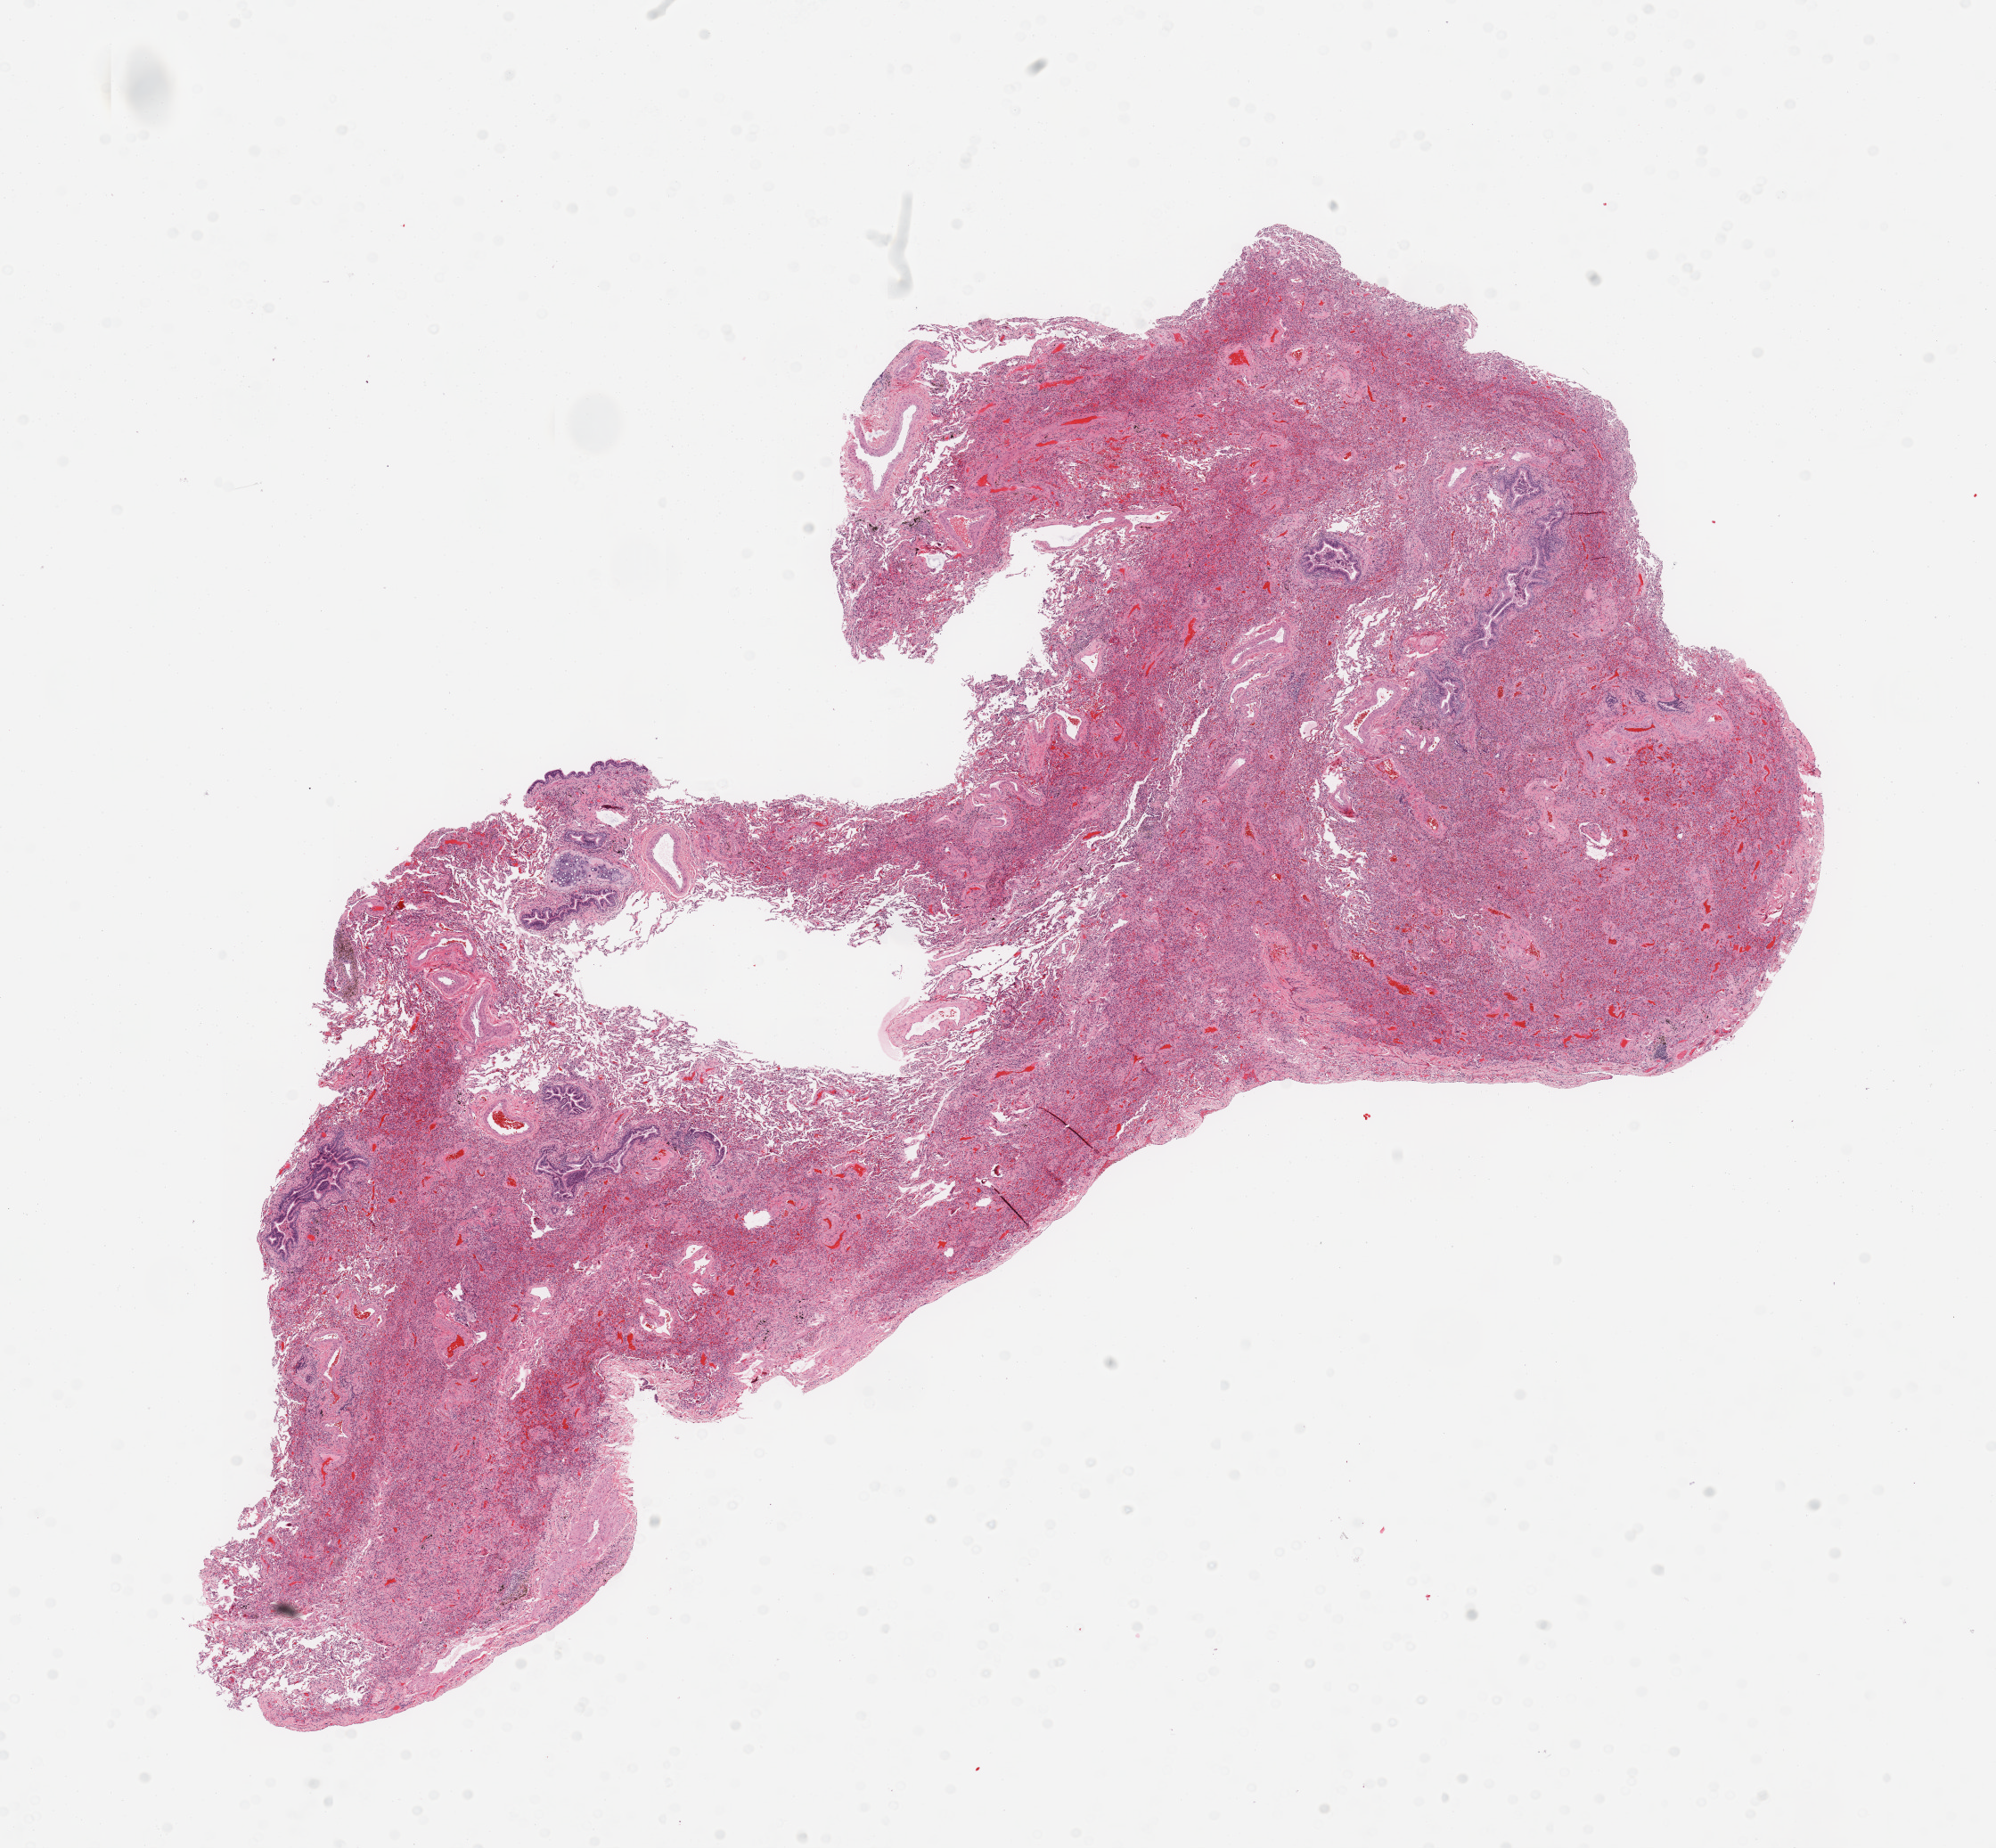
Whole-slide histology image, H&E, shown as a low-resolution overview of the whole scanned area (about 17.7 x 16.4 mm, slide scanned at 20x), normal (non-tumour) tissue sample, sampled site: lung. Male, 58 y/o.
This section: normal (non-tumour) tissue from the same patient. Patient diagnosis: Adenocarcinoma, NOS.